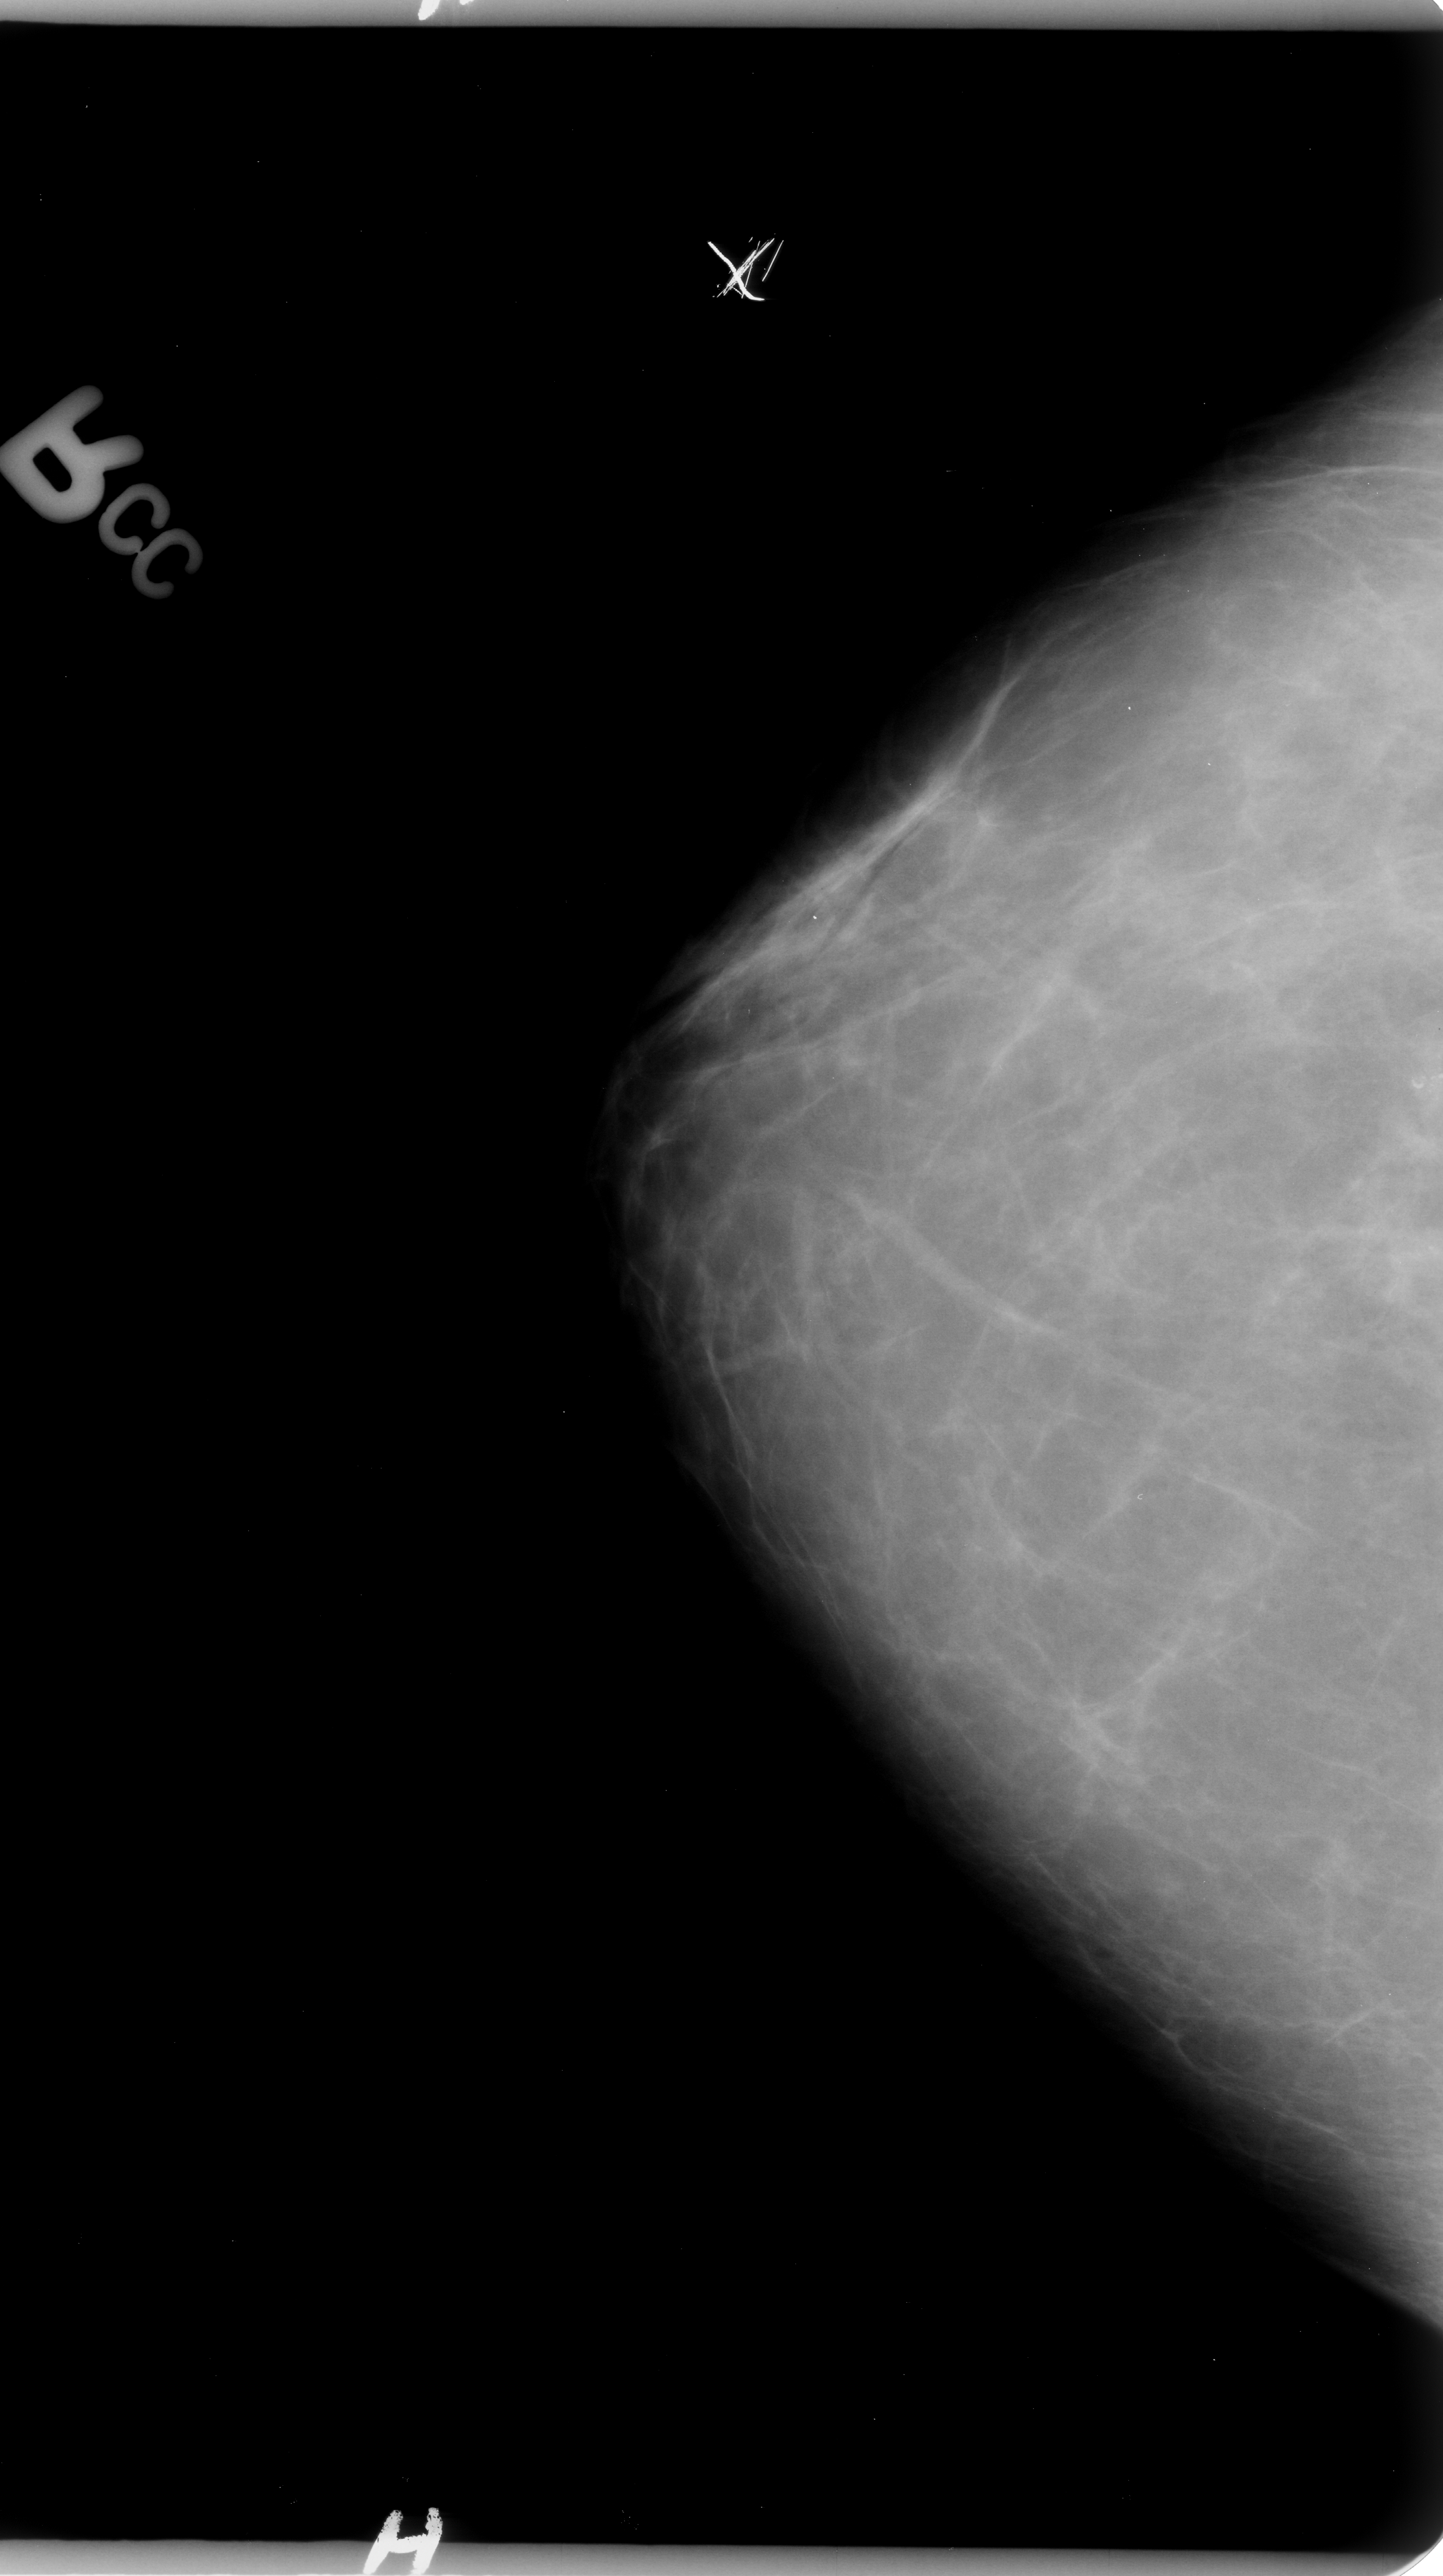
Scanned film-screen mammogram, right breast, craniocaudal (CC) view.
- Calcifications, morphology pleomorphic, distribution clustered; BI-RADS assessment category 4; subtlety rating 4 on a 1 (subtle) to 5 (obvious) scale; pathology (as recorded): malignant.